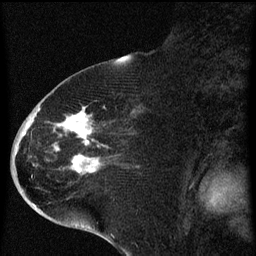
Breast MRI (dynamic contrast-enhanced), one sagittal slice. Position 30 of 60 along the scan axis. Dynamic contrast-enhanced series, image 2 of 4 at this slice position (ordered by acquisition). 1.5 T. TE 4.2 ms, TR 8 ms. 256 × 256 image matrix. Patient: female, 71 years.
Annotated regions visible in this slice (semi-automatically segmented with operator editing):
- analysis volume of interest (the breast-tissue region the enhancement analysis was run in; not a lesion): bounding box [x1, y1, x2, y2] px = [32, 86, 141, 205]
- tumour enhancement mask (voxels above the 70 % enhancement threshold inside the analysis volume of interest): [38, 108, 105, 173]